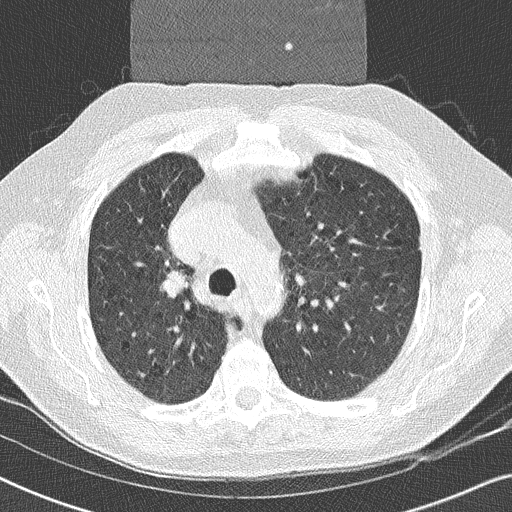
Low-dose screening chest CT, one axial slice. Position 173 of 252 along the scan axis. 120 kVp. Lung window (W 1500 / L -600 HU). 2 mm slice thickness. 512 × 512 image matrix, field of view 330 × 330 mm.
Structures marked on this image (manually delineated by an expert):
- lesion 1 (tumor, upper lobe of right lung): bounding box [x1, y1, x2, y2] px = [164, 273, 186, 297]